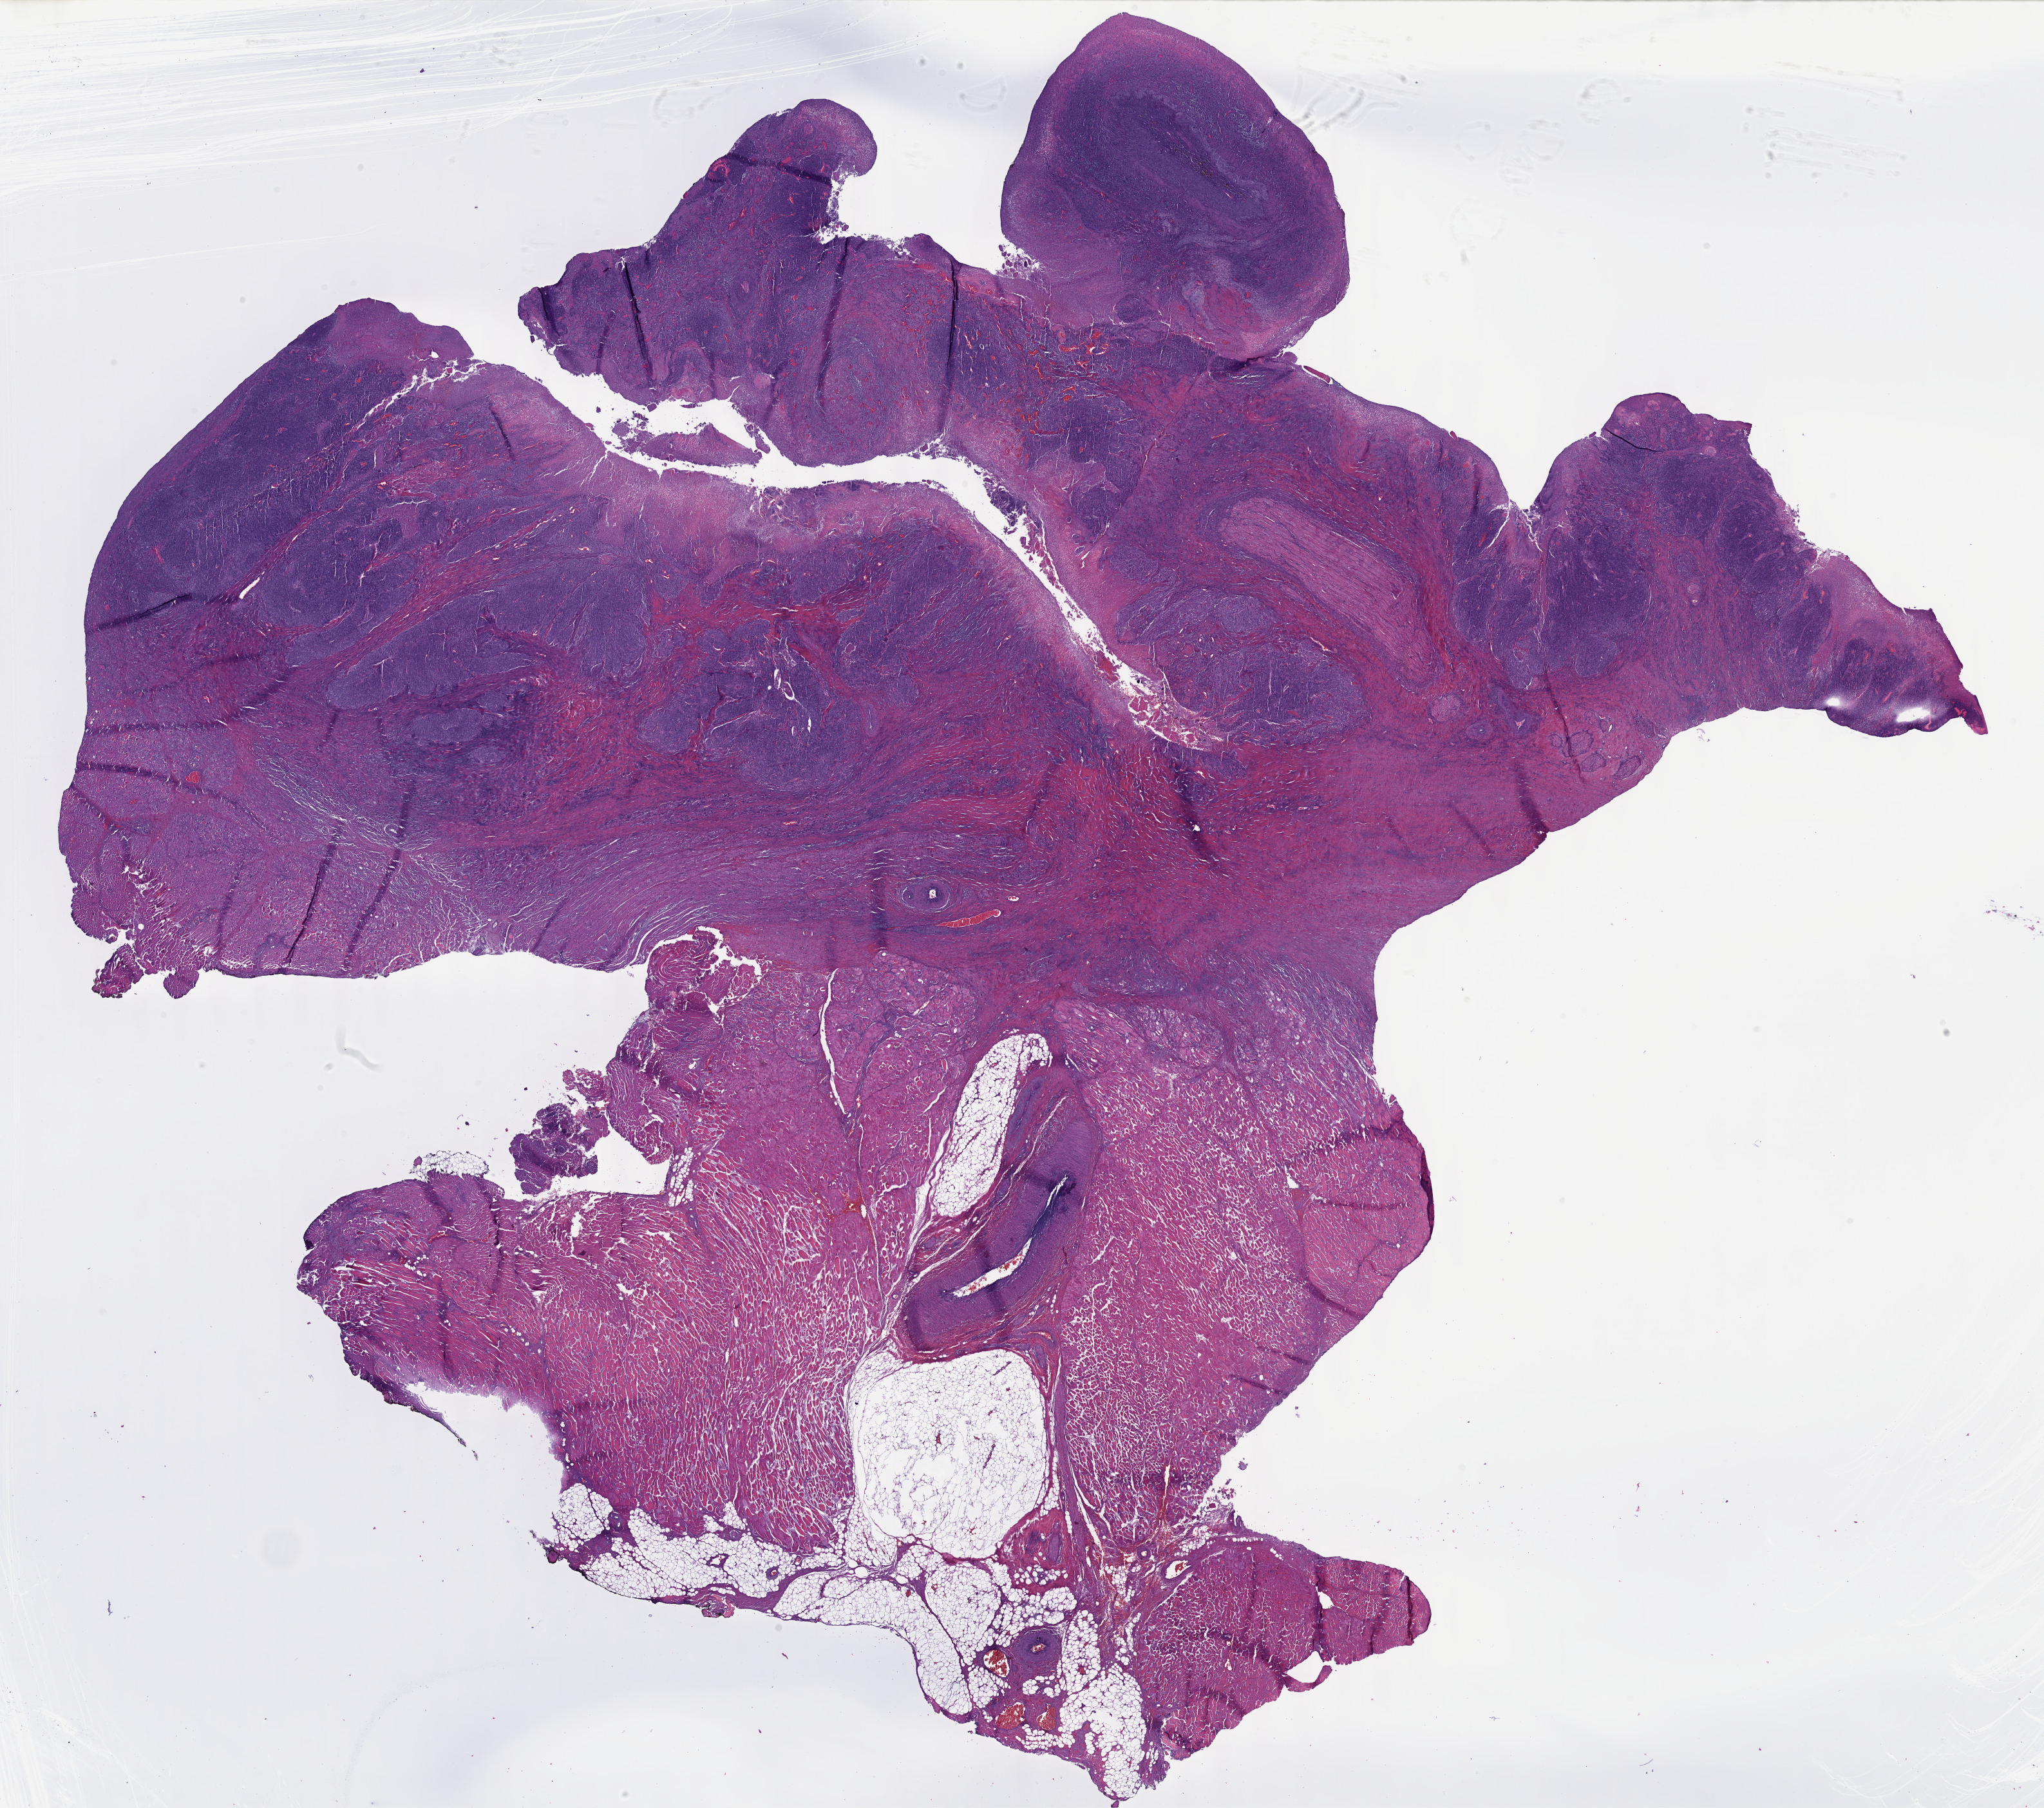
Digitized Hematoxylin and eosin (H&E) stained tissue section (whole slide), a low-resolution overview of the entire scanned area, about 25.7 x 22.7 mm (slide scanned at 40x); formalin-fixed paraffin-embedded (FFPE) diagnostic section; primary tumour sample from the head and neck. Male, age 57 years at initial diagnosis. Histologic grade: G3 (poorly differentiated).
* pathologic diagnosis: Squamous cell carcinoma, NOS (tongue, NOS)
* TNM: T2 N0
* AJCC pathologic stage: II